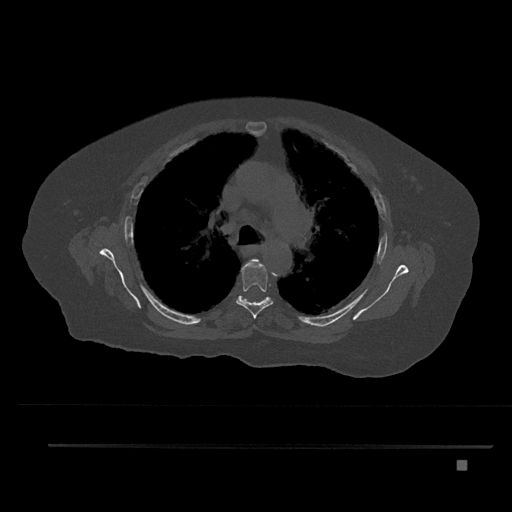
CT including the spine, one axial slice. Bone window (W 1800 / L 400 HU). 512 × 512 image matrix, field of view 437 × 437 mm. Female patient, age 76 years. From the clinical record (not read from this slice): primary cancer: lung; vertebrae with lytic lesions (as recorded): T11, L3.
Structures marked on this image (semi-automatically segmented with operator editing):
- T4 vertebra: bounding box <252,259,259,265> (left, top, right, bottom; pixels)
- T5 vertebra: <236,260,274,319>
- T6 vertebra: <242,298,265,303>